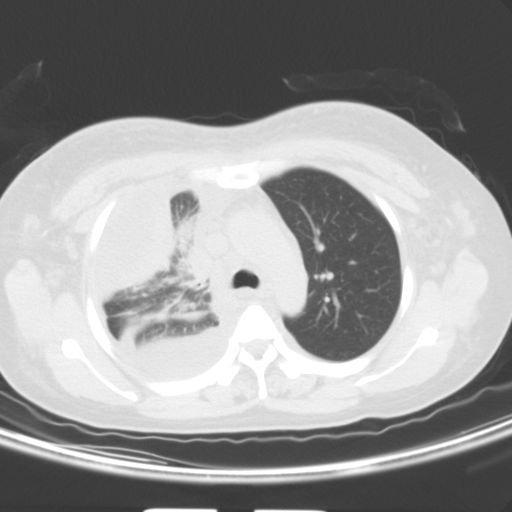
Chest CT, one axial slice; 120 kVp; lung window (W 1500 / L -600 HU); 512 × 512 image matrix, field of view 347 × 347 mm. Patient: female, 36 years. Case-level facts recorded for this patient, not image findings: clinical TNM (as recorded): T1b N2 M0; histopathological grade: G3.
Structures marked on this image (rectangle marked by the reading radiologist):
- lung tumour (recorded histology: adenocarcinoma): bounding box [x1, y1, x2, y2] px = [180, 243, 236, 327]